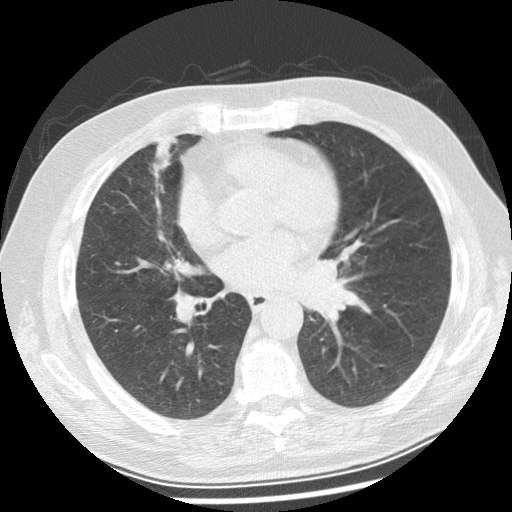
Low-dose screening chest CT, one axial slice; position 125 of 250 along the scan axis; reconstruction kernel STANDARD; lung window (W 1500 / L -600 HU); 2.5 mm slice thickness; 512 × 512 image matrix, field of view 360 × 360 mm.
Annotated regions visible in this slice (expert manual segmentation):
- lesion 1 (tumor, left main bronchus): bounding box <295,258,354,319> (left, top, right, bottom; pixels)